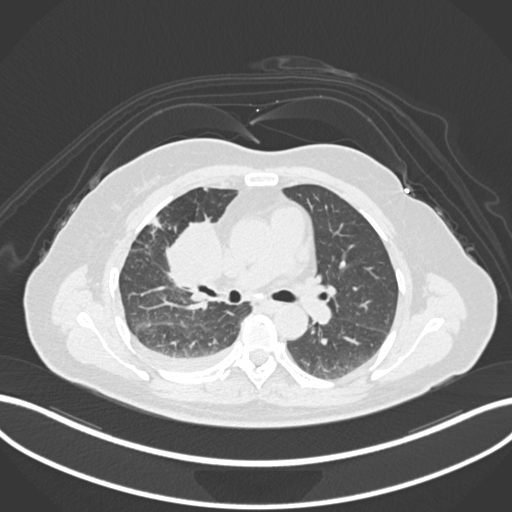
Chest CT, one axial slice. Slice 85 of 172 in the series (ordered by position). Reconstruction kernel B30f. 120 kVp. Lung window (W 1500 / L -600 HU). 1 mm slice thickness. 512 × 512 image matrix, field of view 400 × 400 mm. Patient: female, 52 years. Case-level facts recorded for this patient, not image findings: clinical TNM (as recorded): T3 N1 M1.
Structures marked on this image (bounding box drawn by a radiologist):
- lung tumour (recorded histology: adenocarcinoma): box from (x=165, y=214) to (x=226, y=291) px